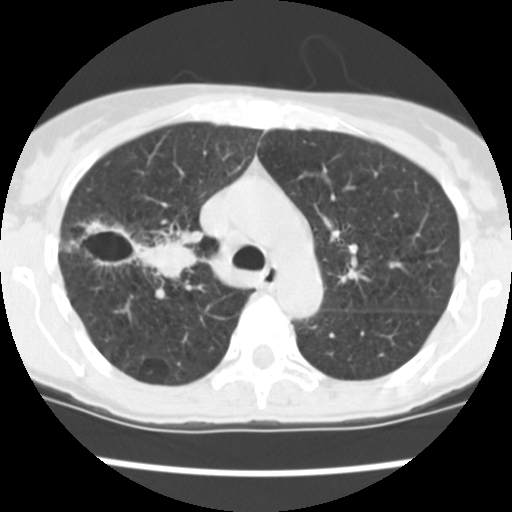
Low-dose screening chest CT, one axial slice; position 171 of 252 along the scan axis; reconstruction kernel STANDARD; lung window (W 1500 / L -600 HU); 2.5 mm slice thickness; 512 × 512 image matrix.
Annotated regions visible in this slice (manually delineated by an expert):
- lesion 2 (tumor, lower lobe of right lung): bounding box (x1, y1, x2, y2) in pixels: (83, 220, 203, 280)